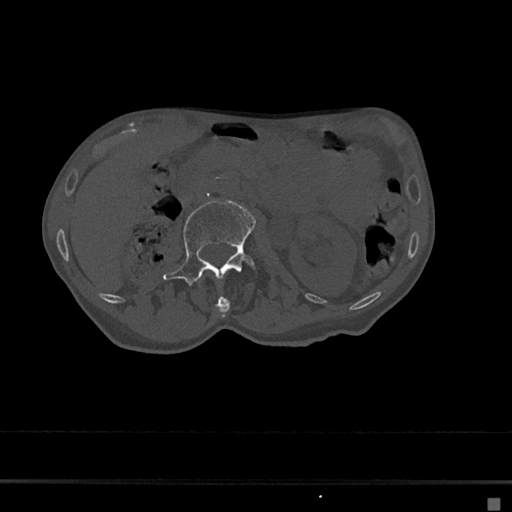
CT including the spine, one axial slice. Slice 18 of 797 in the series (ordered by position). Reconstruction kernel Br40s/3. 120 kVp. Bone window (W 1800 / L 400 HU). 0.5 mm slice thickness. 512 × 512 image matrix, field of view 360 × 360 mm. Patient: female, 68 years. From the clinical record (not read from this slice): primary cancer: renal.
Structures marked on this image (semi-automatic segmentation, software-assisted and operator-edited):
- L1 vertebra: bounding box [x1, y1, x2, y2] px = [214, 295, 230, 319]
- L2 vertebra: [163, 200, 257, 288]